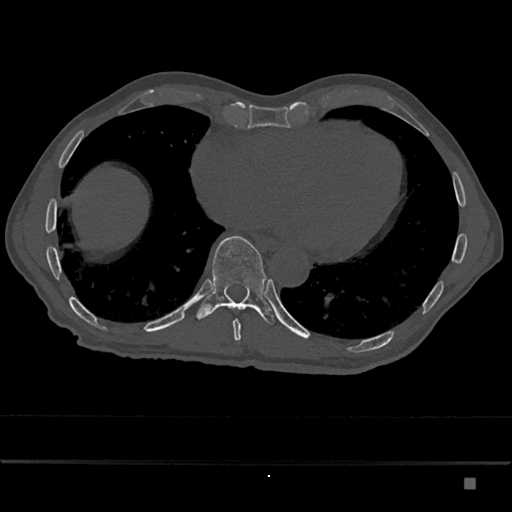
CT including the spine, one axial slice. Position 760 of 797 along the scan axis. Reconstruction kernel Br40s/3. 120 kVp. Bone window (W 1800 / L 400 HU). 0.5 mm slice thickness. 512 × 512 image matrix, field of view 390 × 390 mm. Male patient, age 72 years. Case-level facts recorded for this patient, not image findings: primary cancer: prostate.
Annotated regions visible in this slice (semi-automatic segmentation, software-assisted and operator-edited):
- T10 vertebra: box from (x=196, y=236) to (x=275, y=325) px
- T9 vertebra: (x=233, y=309)–(x=245, y=341)